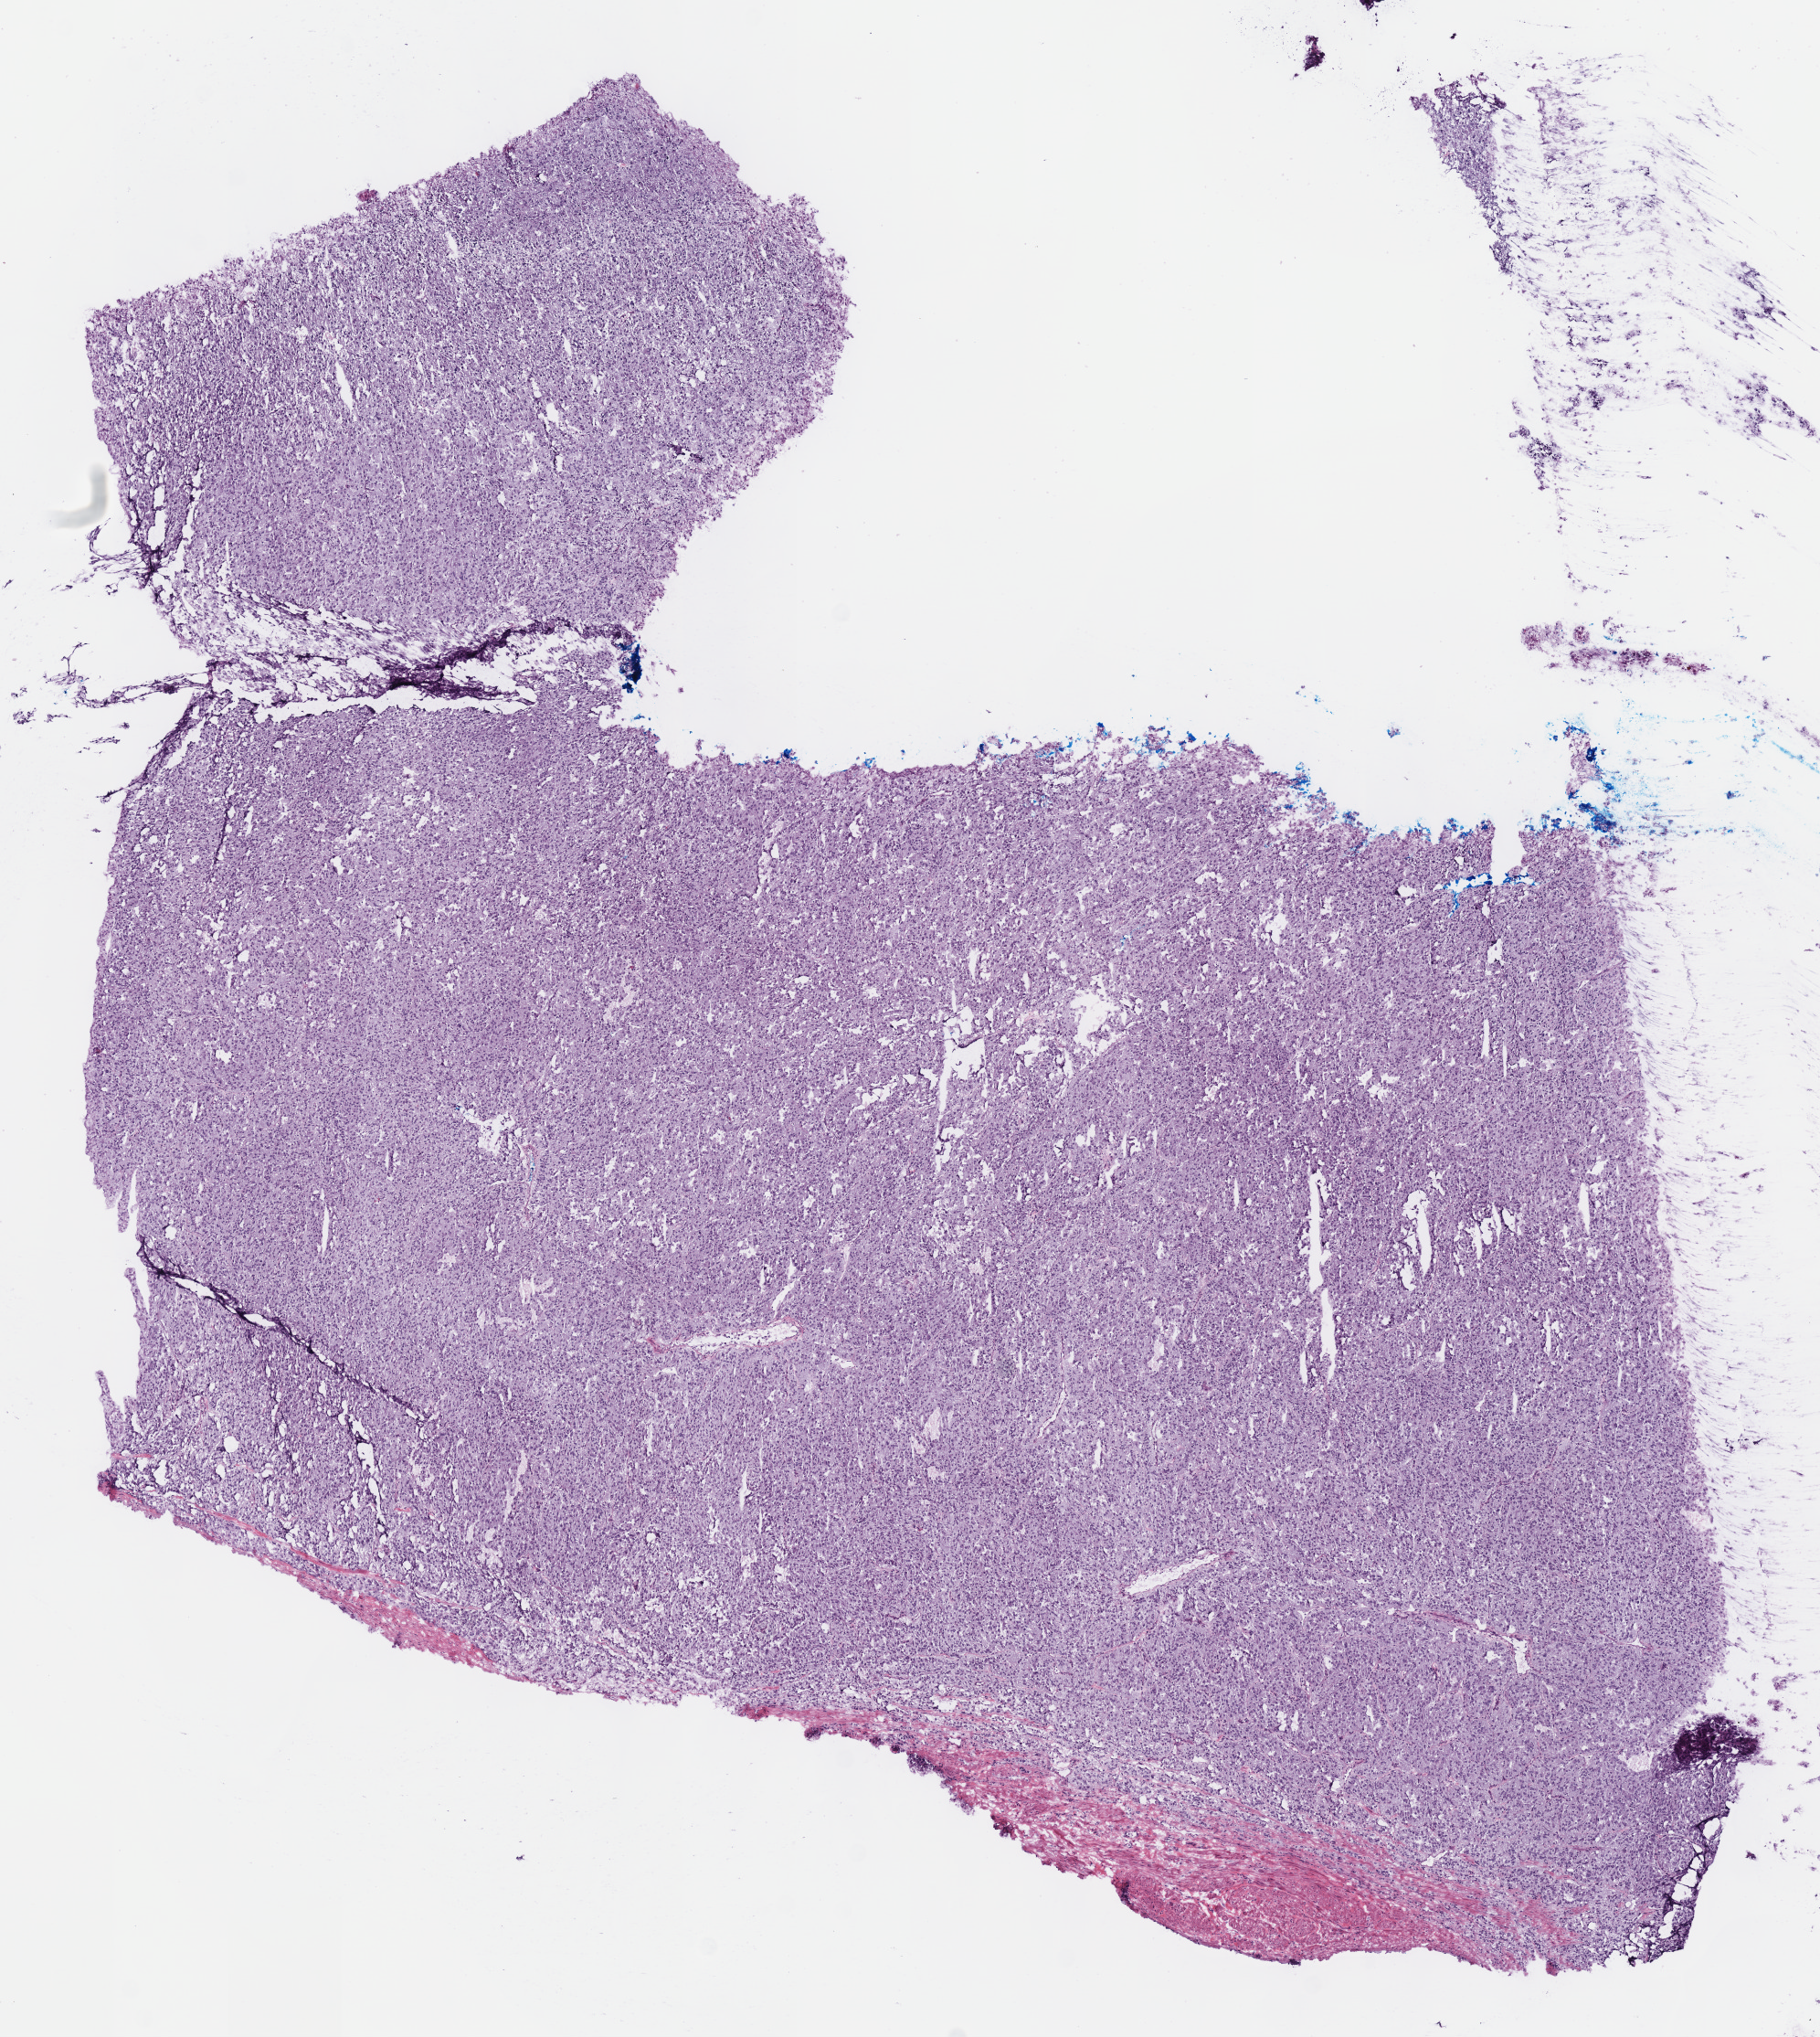
Whole-slide histology image, Hematoxylin and eosin (H&E) stained — a low-resolution overview of the entire scanned area, about 7.8 x 8.8 mm (from a 40x scan), frozen section from the top of the tissue portion, primary tumour sample from the adrenal gland. Male patient; age at initial diagnosis 39 years. Slide review estimates, as recorded: tumour cells 100%, tumour nuclei 80%, normal cells 0%, stromal cells 0%, necrosis 0%. Inflammatory infiltration, as recorded: lymphocyte infiltration 1%, monocyte infiltration 0%, neutrophil infiltration 0%.
* laterality: right
* histologic diagnosis: Pheochromocytoma, malignant